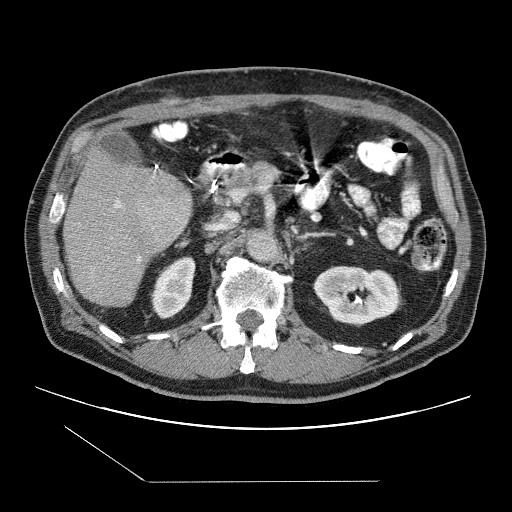
Contrast-enhanced abdominal CT (liver protocol), one axial slice; position 43 of 109 along the scan axis; one of 2 acquisitions stored at this slice position; soft-tissue window (W 400 / L 40 HU); 2.5 mm slice thickness; 512 × 512 image matrix, field of view 400 × 400 mm. From the clinical record (not read from this slice): diagnosis: hepatocellular carcinoma (patient treated with transarterial chemoembolisation; whether this scan precedes or follows treatment is not stated here); TNM stage (as recorded): Stage-IIIB; Child-Pugh class: A; tumour differentiation: well differentiated; tumour nodularity: multinodular.
Annotated regions visible in this slice (semi-automatic segmentation, software-assisted and operator-edited):
- liver parenchyma outside the tumour (the mass and vessels are separate outlines, so this box may not span the whole liver): bounding box <64,148,192,306> (left, top, right, bottom; pixels)
- liver vessels: <114,200,184,262>